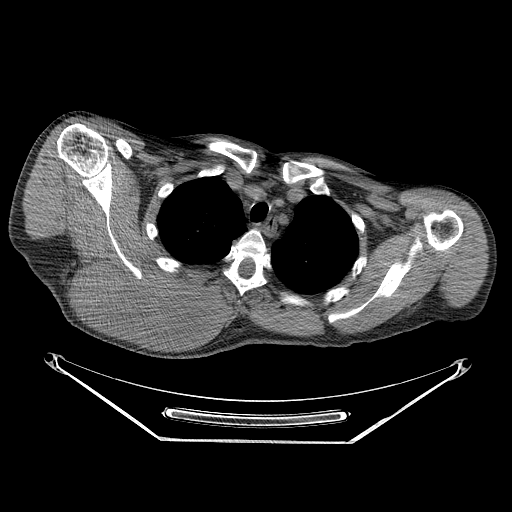
CT of an extremity soft-tissue mass (from a PET/CT study), one axial slice. Position 195 of 267 along the scan axis. Reconstruction kernel STANDARD. 140 kVp. Soft-tissue window (W 400 / L 40 HU). 512 × 512 image matrix, field of view 500 × 500 mm. Male patient. From the clinical record (not read from this slice): histological type: pleiomorphic spindle cell undifferentiated; grade: high; site of the primary tumour: right parascapusular.
Annotated regions visible in this slice (expert contour drawn on MRI and transferred to this co-registered scan by the dataset authors):
- gross tumour volume including surrounding oedema: bounding box [x1, y1, x2, y2] px = [75, 262, 234, 337]
- gross tumour volume (mass): [75, 262, 216, 336]